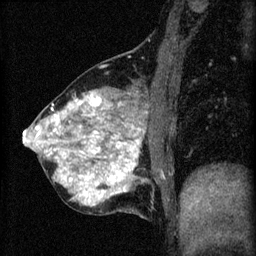
Breast MRI (dynamic contrast-enhanced), one sagittal slice. 3 images stored at this slice position (order not interpretable as contrast timing). 1.5 T. TE 4.2 ms, TR 8.2 ms. 2 mm slice thickness. 256 × 256 image matrix, field of view 180 × 180 mm. Female patient, age 40 years.
Annotated regions visible in this slice (semi-automatic segmentation, software-assisted and operator-edited):
- analysis volume of interest (the breast-tissue region the enhancement analysis was run in; not a lesion): box from (x=24, y=82) to (x=171, y=219) px
- tumour enhancement mask (voxels above the 70 % enhancement threshold inside the analysis volume of interest): (x=24, y=92)–(x=141, y=207)